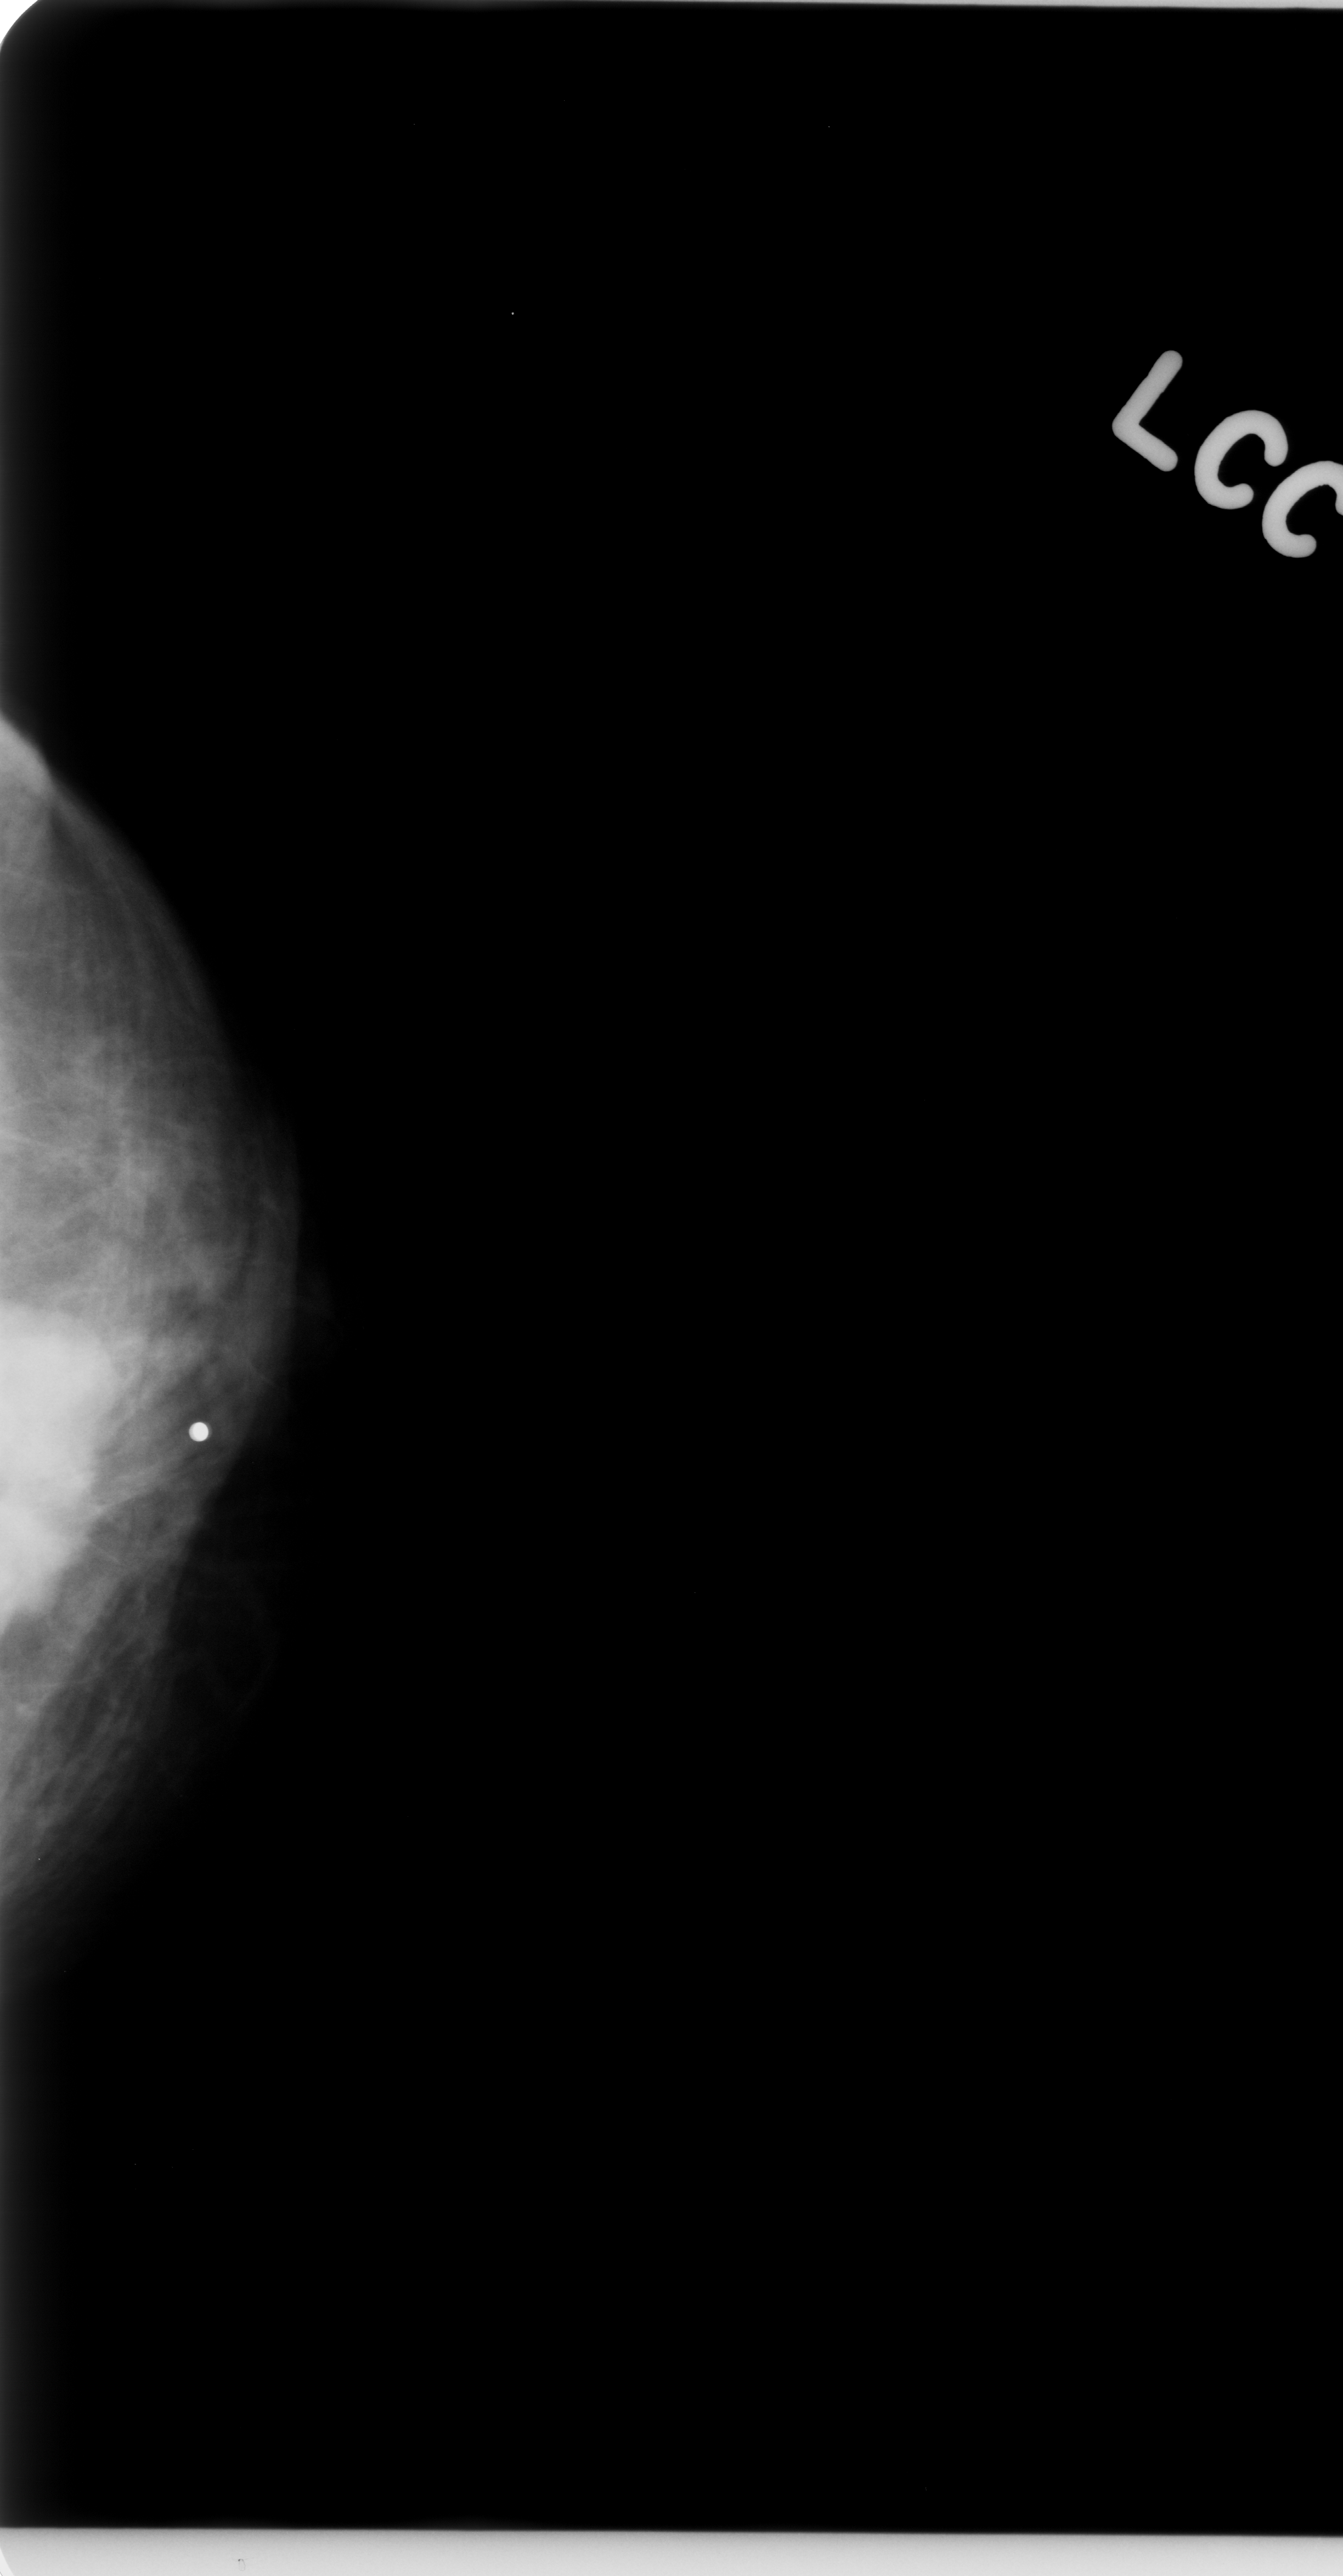
Mammogram (digitized film), left breast, CC view, BI-RADS breast density category 2 (scale 1–4).
Mass, shape irregular, margins microlobulated; BI-RADS assessment category 5; subtlety rating 5 on a 1 (subtle) to 5 (obvious) scale; pathology result (as recorded, not read from the image): malignant.